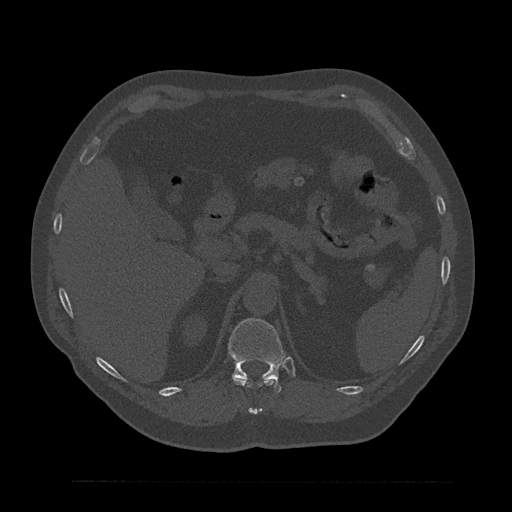
CT including the spine, one axial slice. Position 256 of 797 along the scan axis. Reconstruction kernel Br40s/3. 120 kVp. Bone window (W 1800 / L 400 HU). 512 × 512 image matrix. Patient: male, 61 years. Case-level facts recorded for this patient, not image findings: primary cancer: prostate.
Annotated regions visible in this slice (semi-automatically segmented with operator editing):
- T11 vertebra: box from (x=232, y=376) to (x=275, y=415) px
- T12 vertebra: (x=228, y=318)–(x=285, y=393)